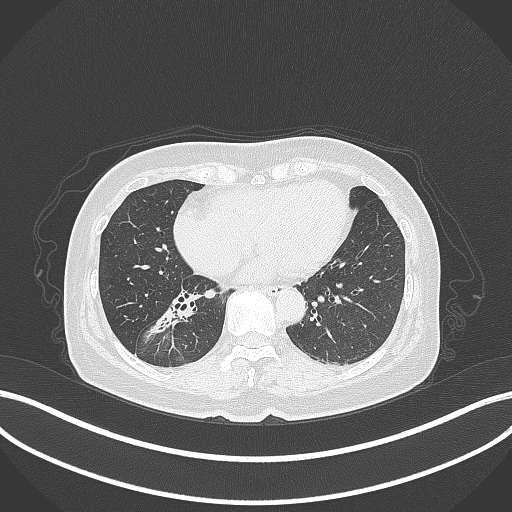
Chest CT, one axial slice; position 149 of 429 along the scan axis; 120 kVp; lung window (W 1500 / L -600 HU); 512 × 512 image matrix, field of view 400 × 400 mm. Female patient, age 67 years. From the clinical record (not read from this slice): clinical TNM (as recorded): T1c N1 M0.
Outlined on this slice (rectangle marked by the reading radiologist):
- lung tumour (recorded histology: adenocarcinoma): bounding box (x1, y1, x2, y2) in pixels: (142, 295, 200, 340)